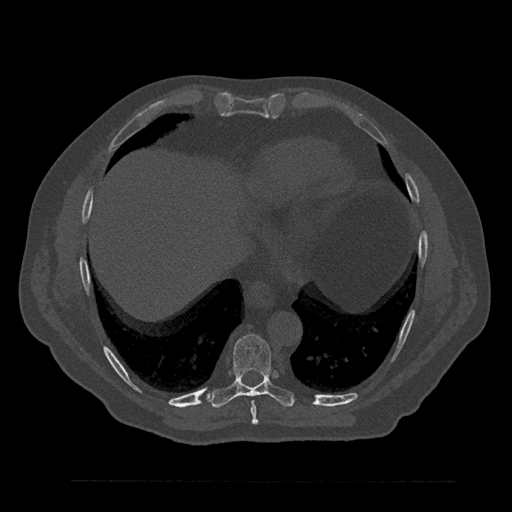
CT including the spine, one axial slice; reconstruction kernel Br40s/3; bone window (W 1800 / L 400 HU); 512 × 512 image matrix, field of view 430 × 430 mm. Patient: male, 61 years. Case-level facts recorded for this patient, not image findings: primary cancer: prostate.
Structures marked on this image (semi-automatic segmentation, software-assisted and operator-edited):
- T8 vertebra: bounding box (x1, y1, x2, y2) in pixels: (251, 400, 259, 425)
- T9 vertebra: (208, 334, 295, 408)